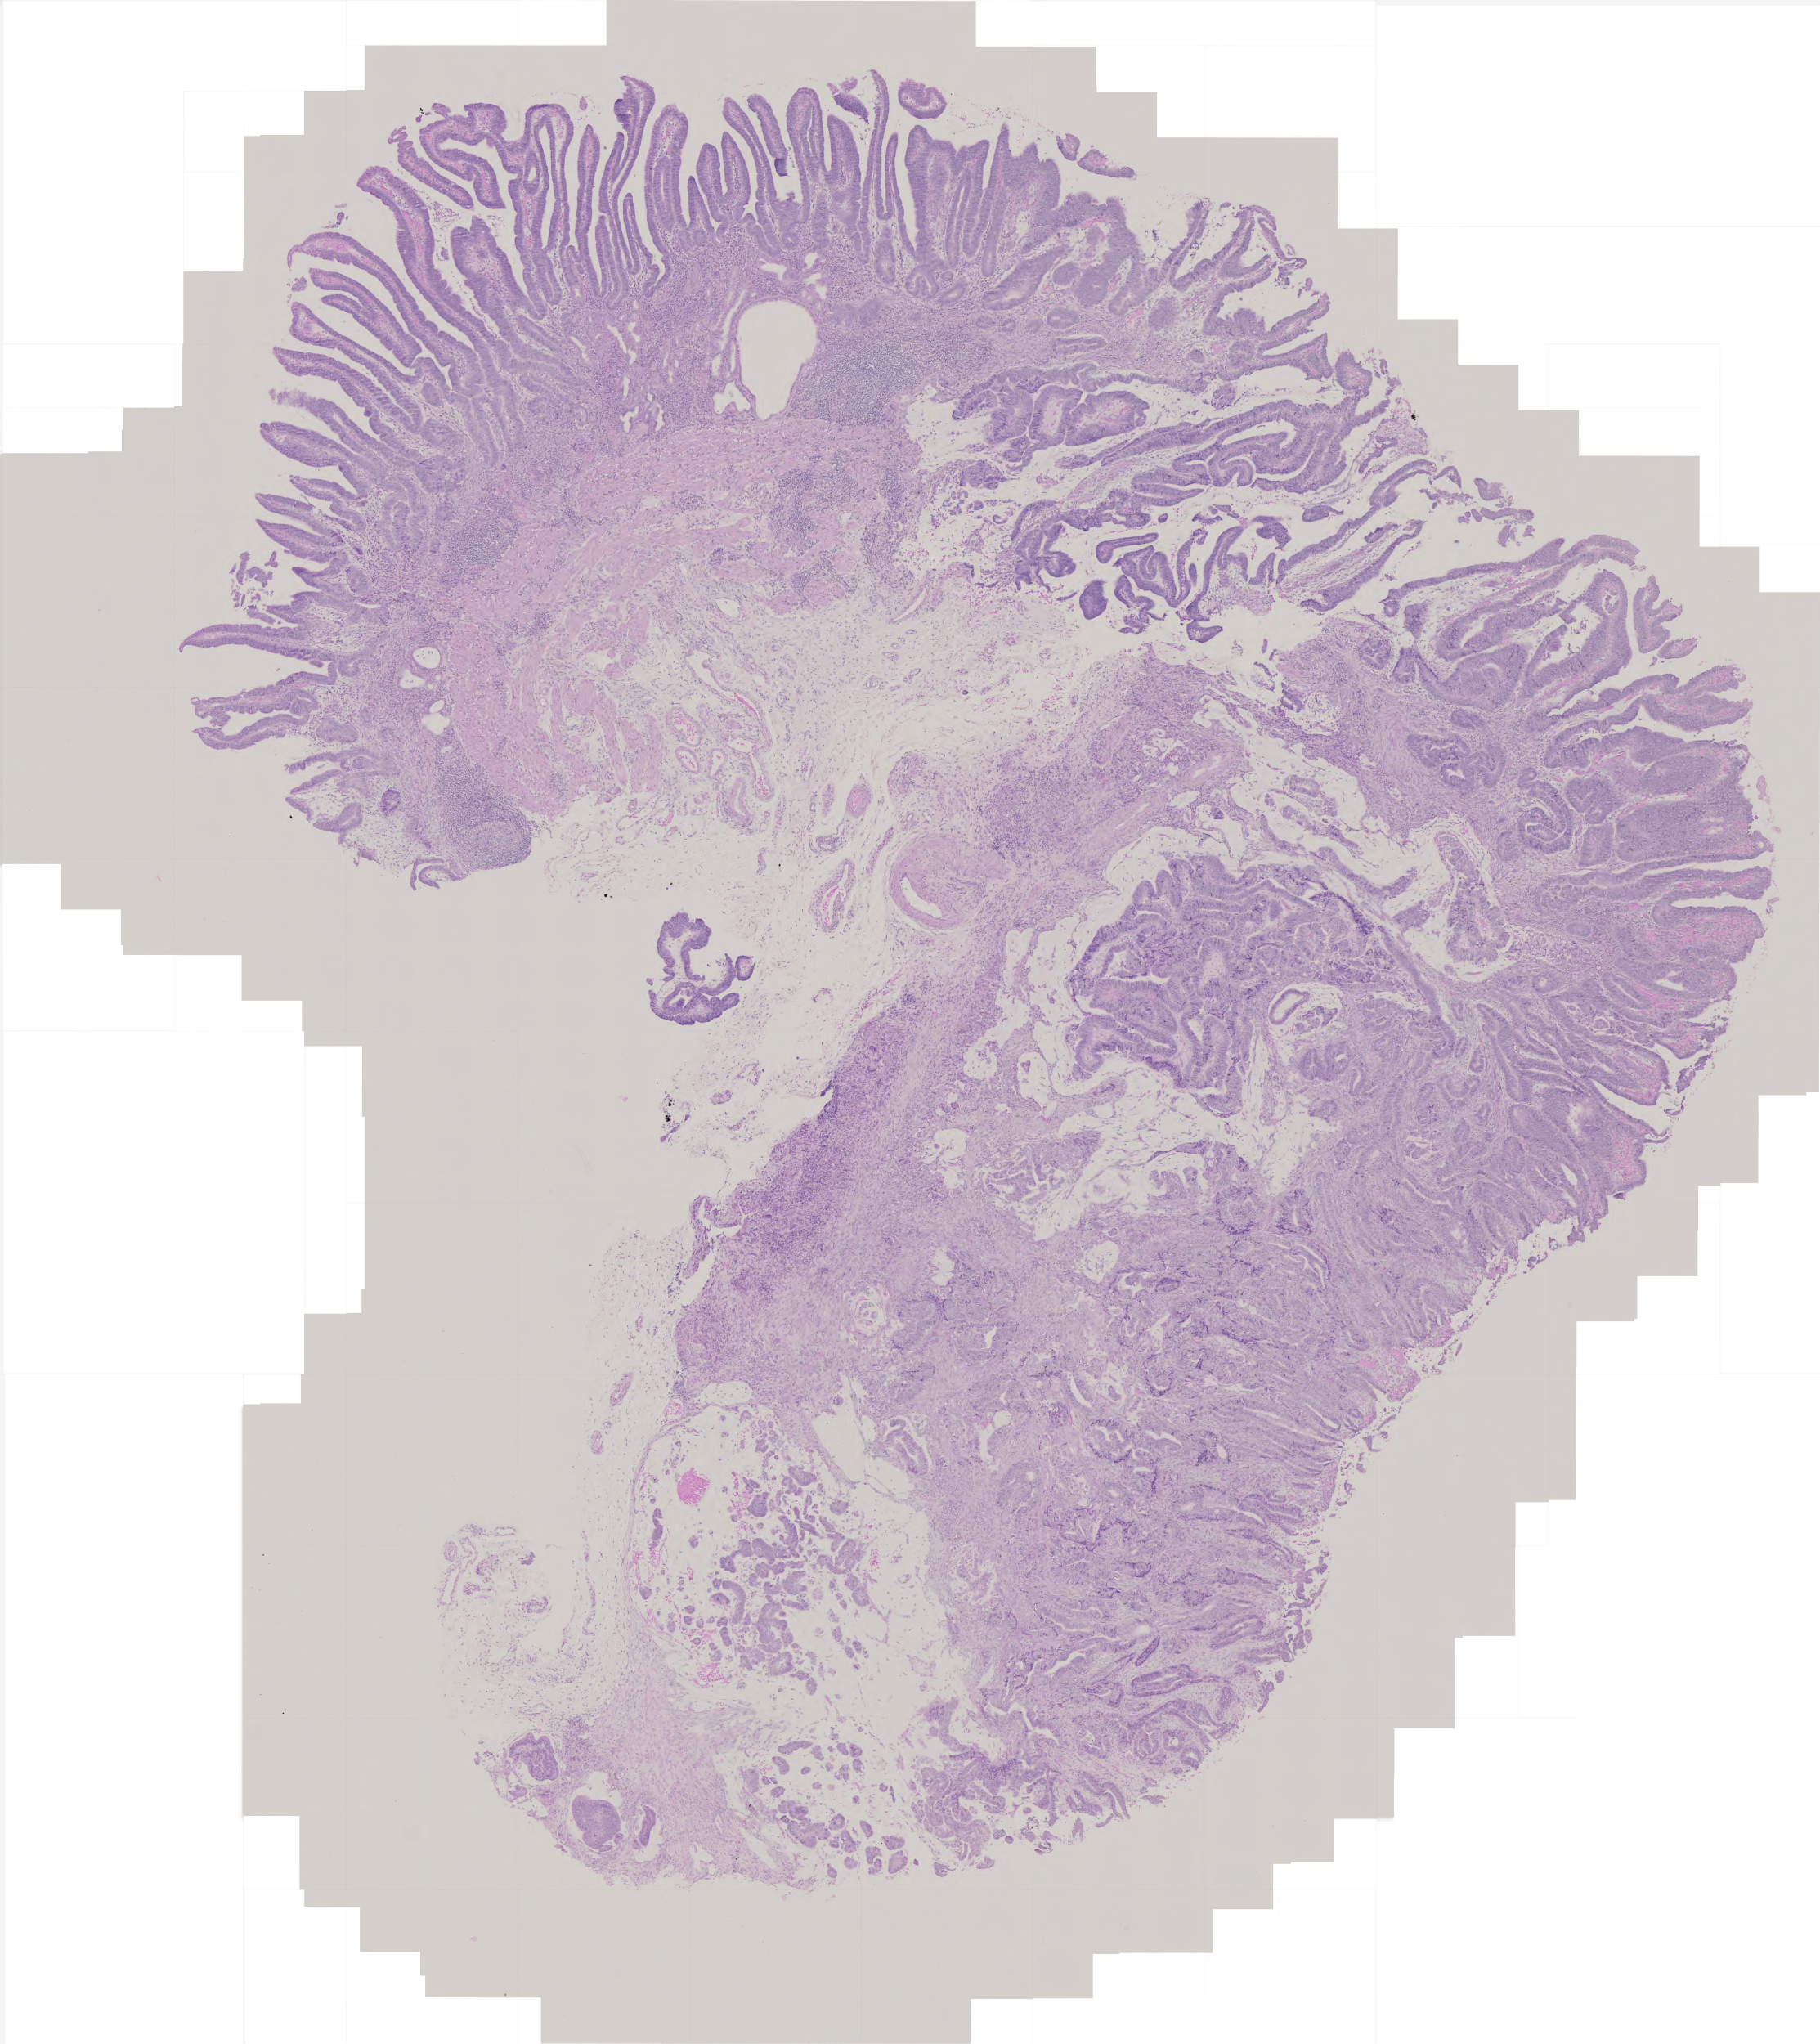
Whole-slide histology image, H&E, low-resolution overview of the scanned area, about 4.5 x 5.0 mm; formalin-fixed paraffin-embedded (FFPE) diagnostic section; sample: primary tumour, stomach. Male, age 73 years at initial diagnosis. Histologic grade: G2 (moderately differentiated).
AJCC pathologic stage: IA. Pathologic diagnosis: Adenocarcinoma, intestinal type (gastric antrum). Lymph nodes positive (case pathology): 0 of 15 examined.